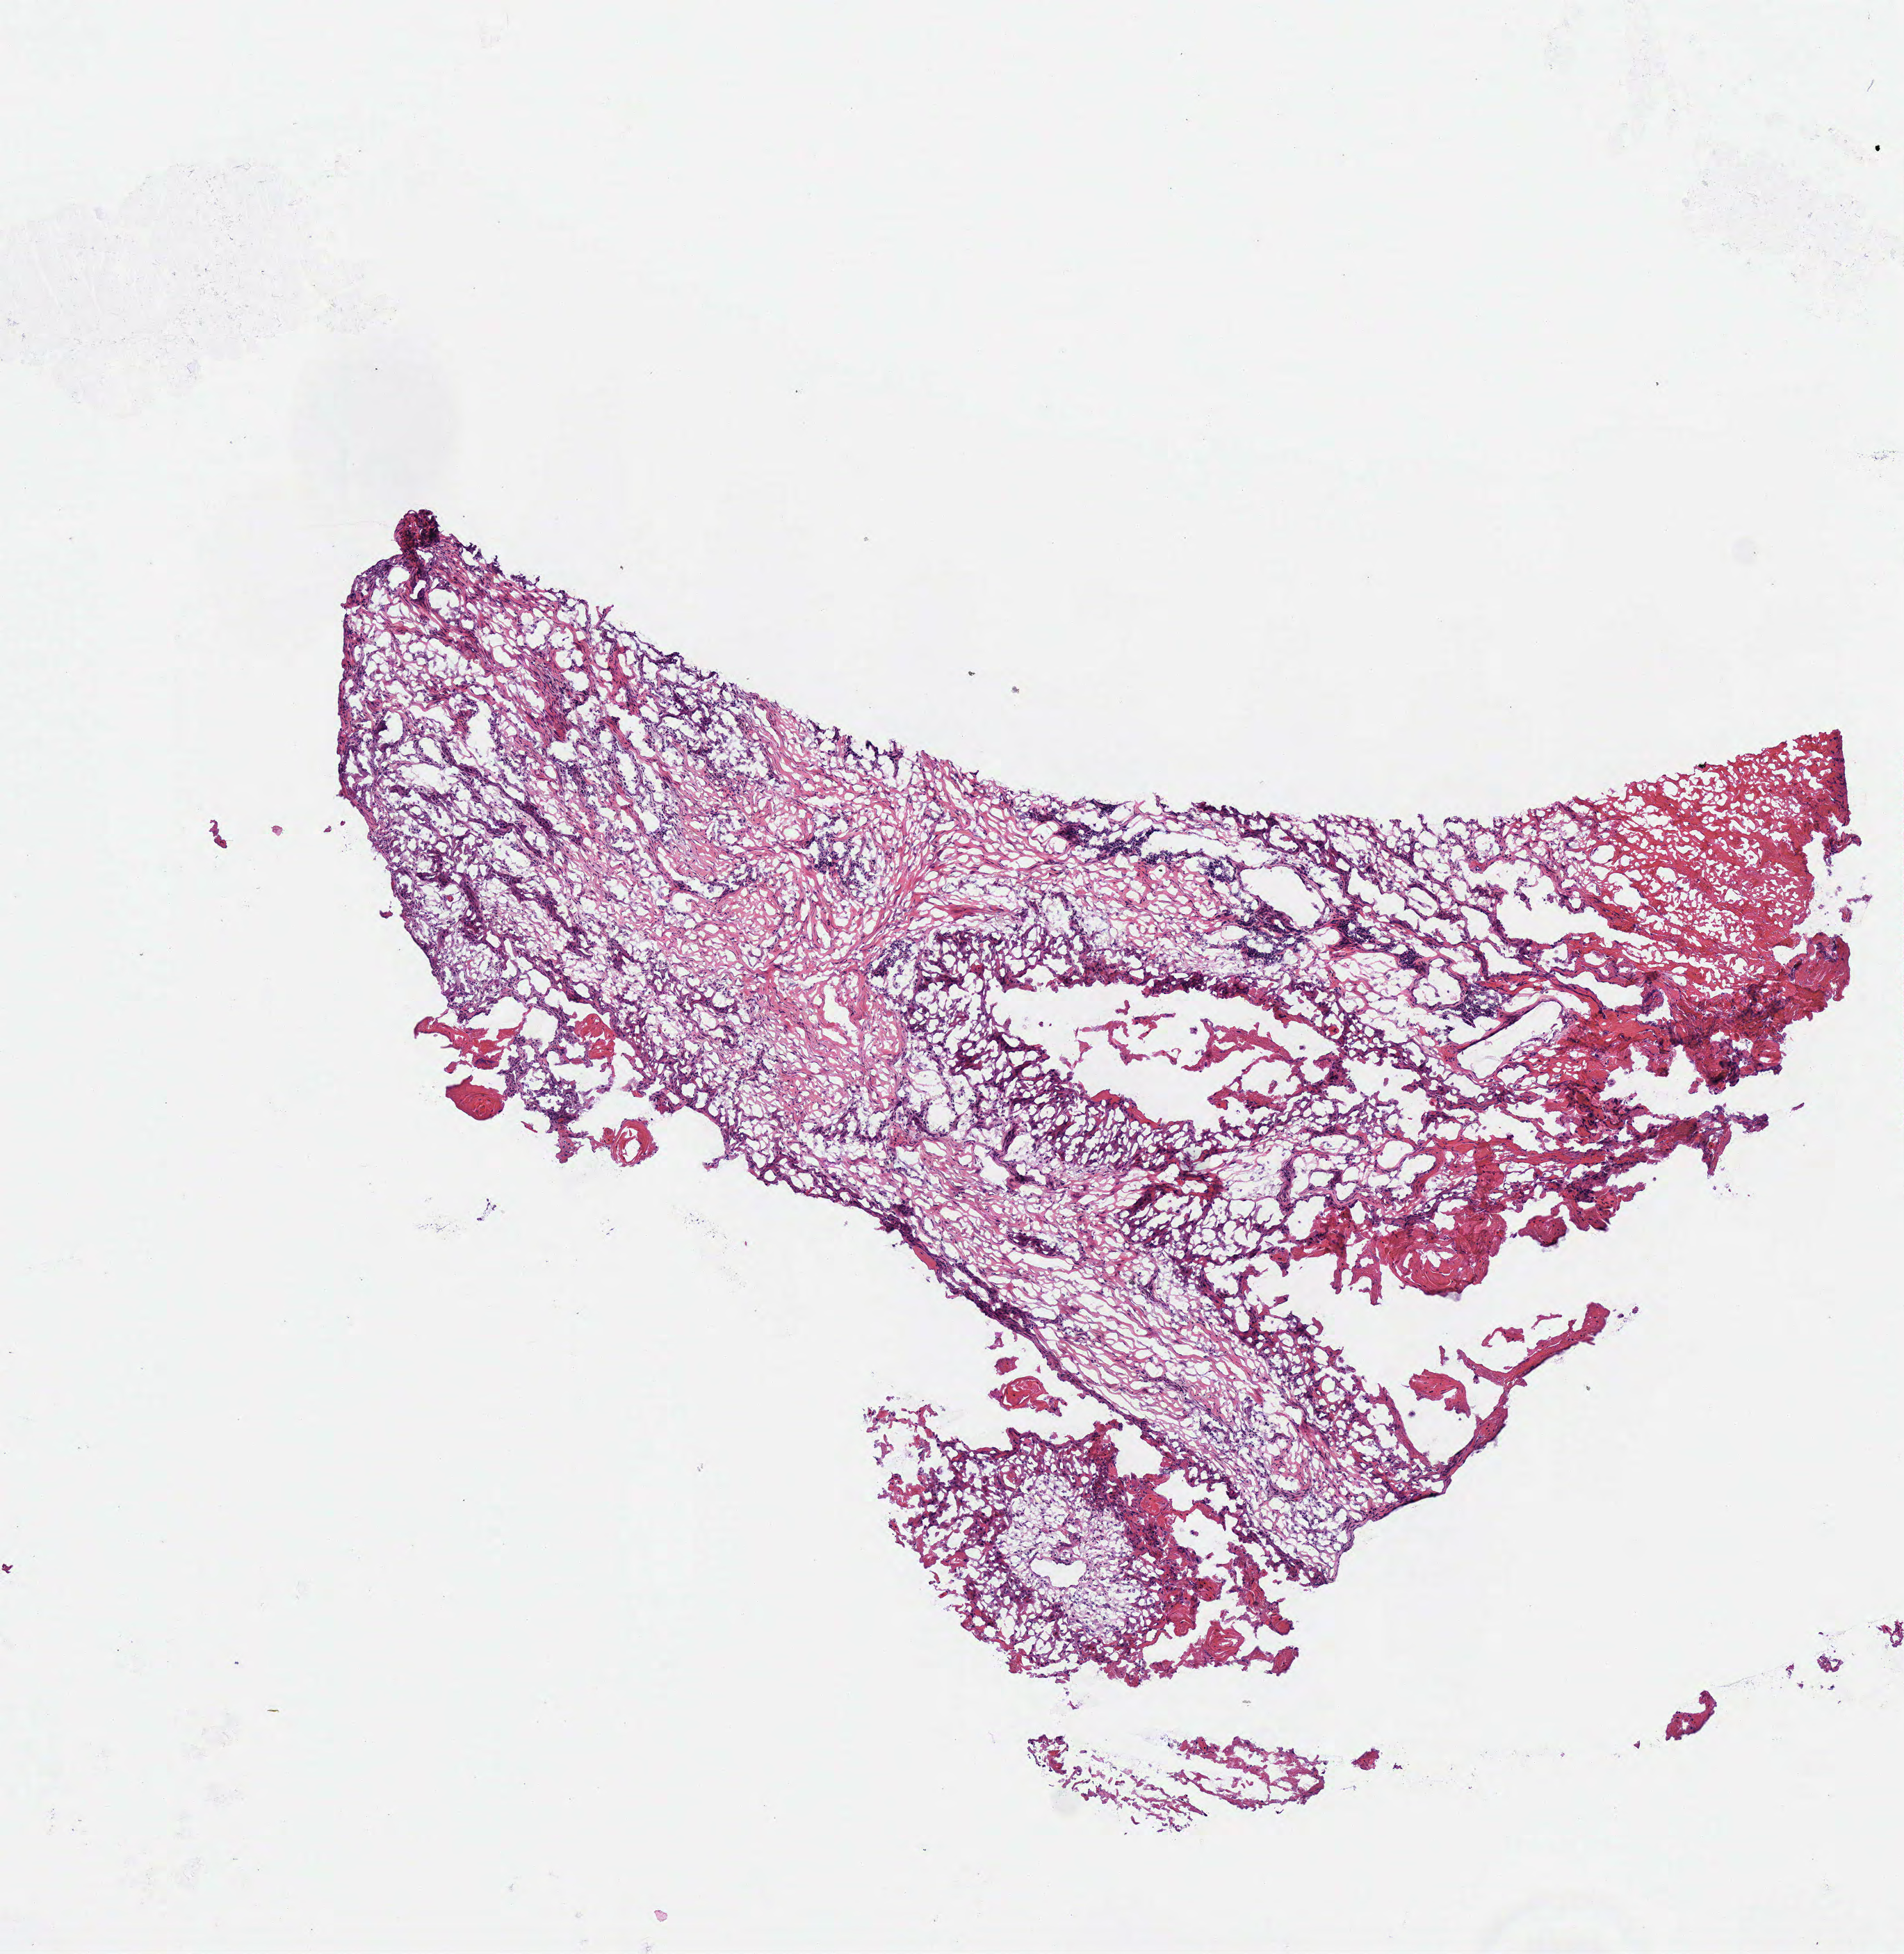
Whole-slide histology image, H&E-stained — shown as a low-resolution overview of the whole scanned area (about 5.4 x 5.5 mm, slide scanned at 40x), frozen section from the bottom of the tissue portion, primary tumour sample from the head and neck. Male, age 39 years at initial diagnosis. Histologic grade: G2 (moderately differentiated). Pathologist review of this section (percent, as recorded): tumour cells 62%, tumour nuclei 50%, normal cells 0%, stromal cells 30%, necrosis 8%.
AJCC pathologic stage: II. Pathologic diagnosis: Squamous cell carcinoma, NOS (overlapping lesion of lip, oral cavity and pharynx).